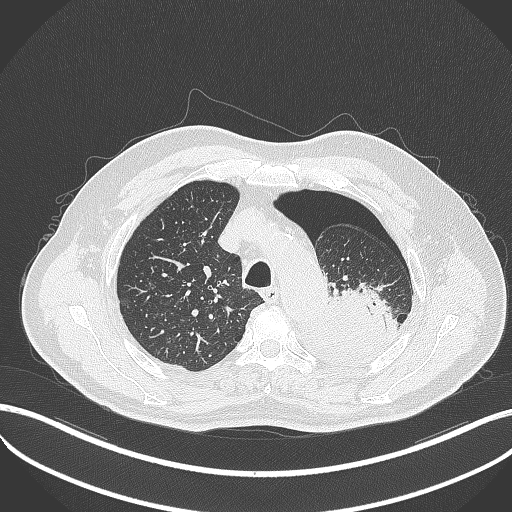
Chest CT, one axial slice; position 391 of 464 along the scan axis; reconstruction kernel B70f; 120 kVp; lung window (W 1500 / L -600 HU); 1 mm slice thickness; 512 × 512 image matrix. Patient: male, 76 years. Case-level facts recorded for this patient, not image findings: clinical TNM (as recorded): T3 N0 M1b.
Outlined on this slice (bounding box drawn by a radiologist):
- lung tumour (recorded histology: adenocarcinoma): bounding box [x1, y1, x2, y2] px = [315, 285, 398, 362]